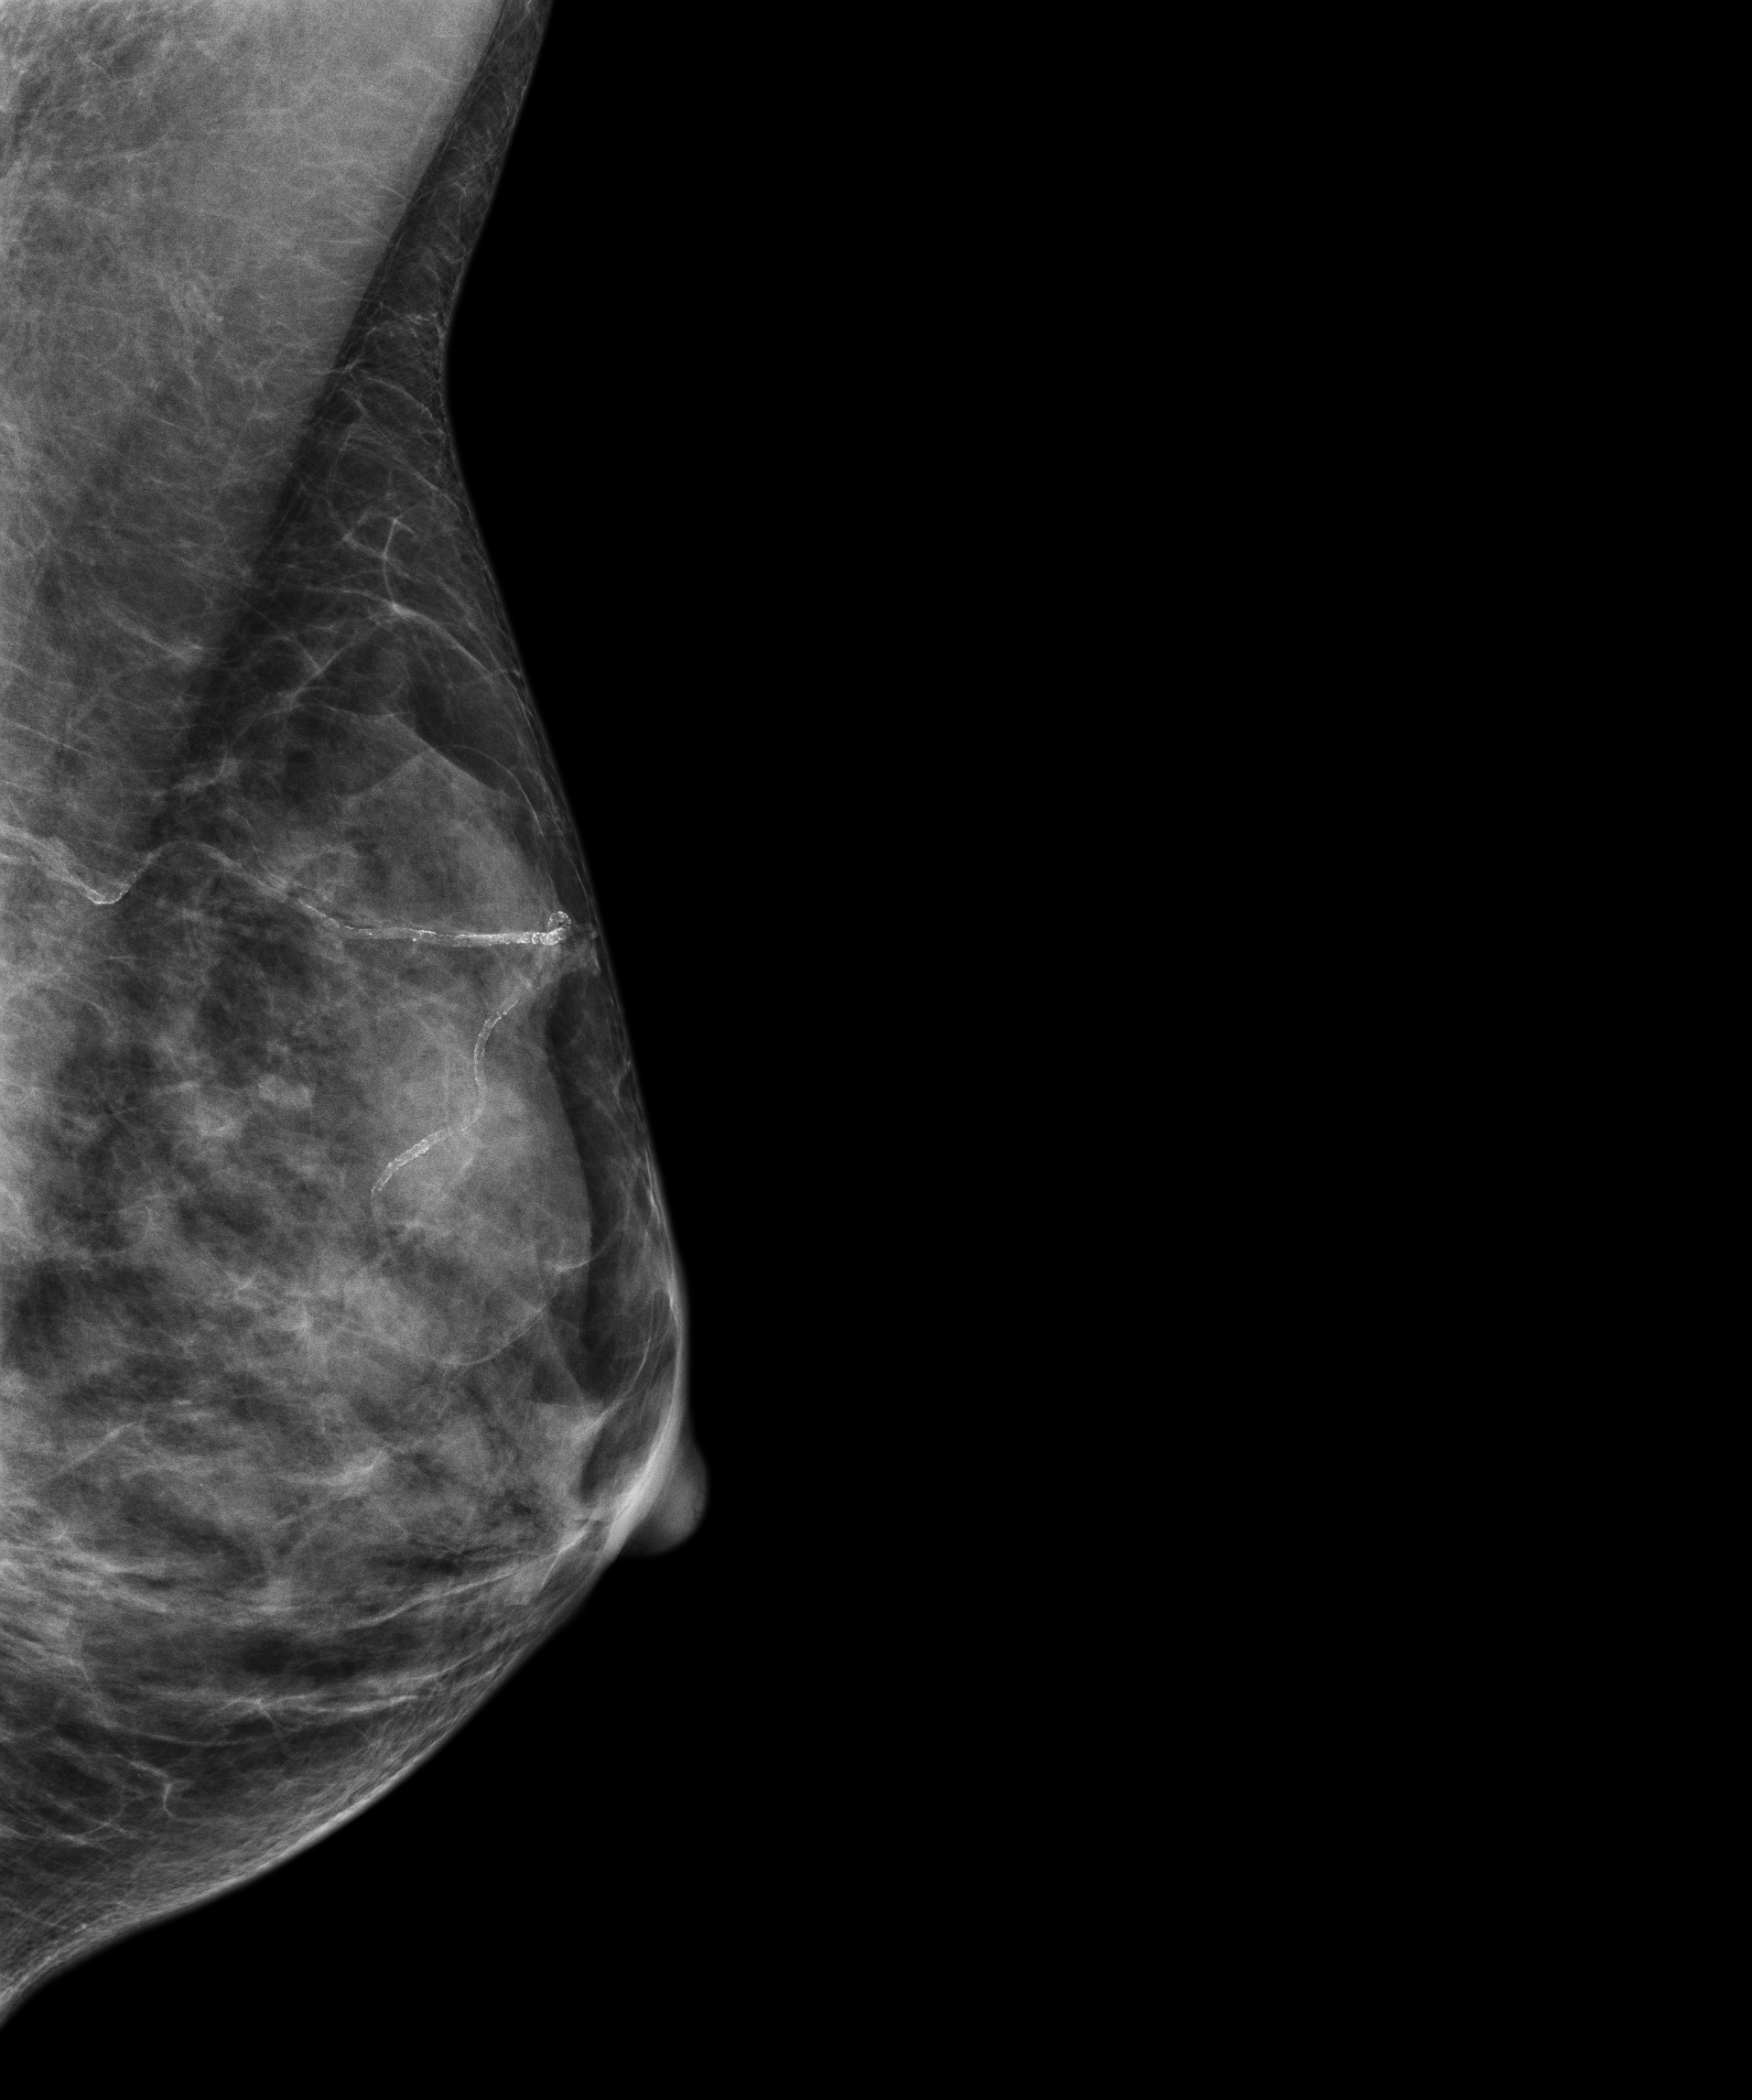
Screening examination, compressed breast thickness 30 mm, system: Senographe Essential ADS_56.21.3. Female patient, age 60 years.
Image type: full-field digital mammogram. Breast: left. Projection: mediolateral oblique (MLO) view.